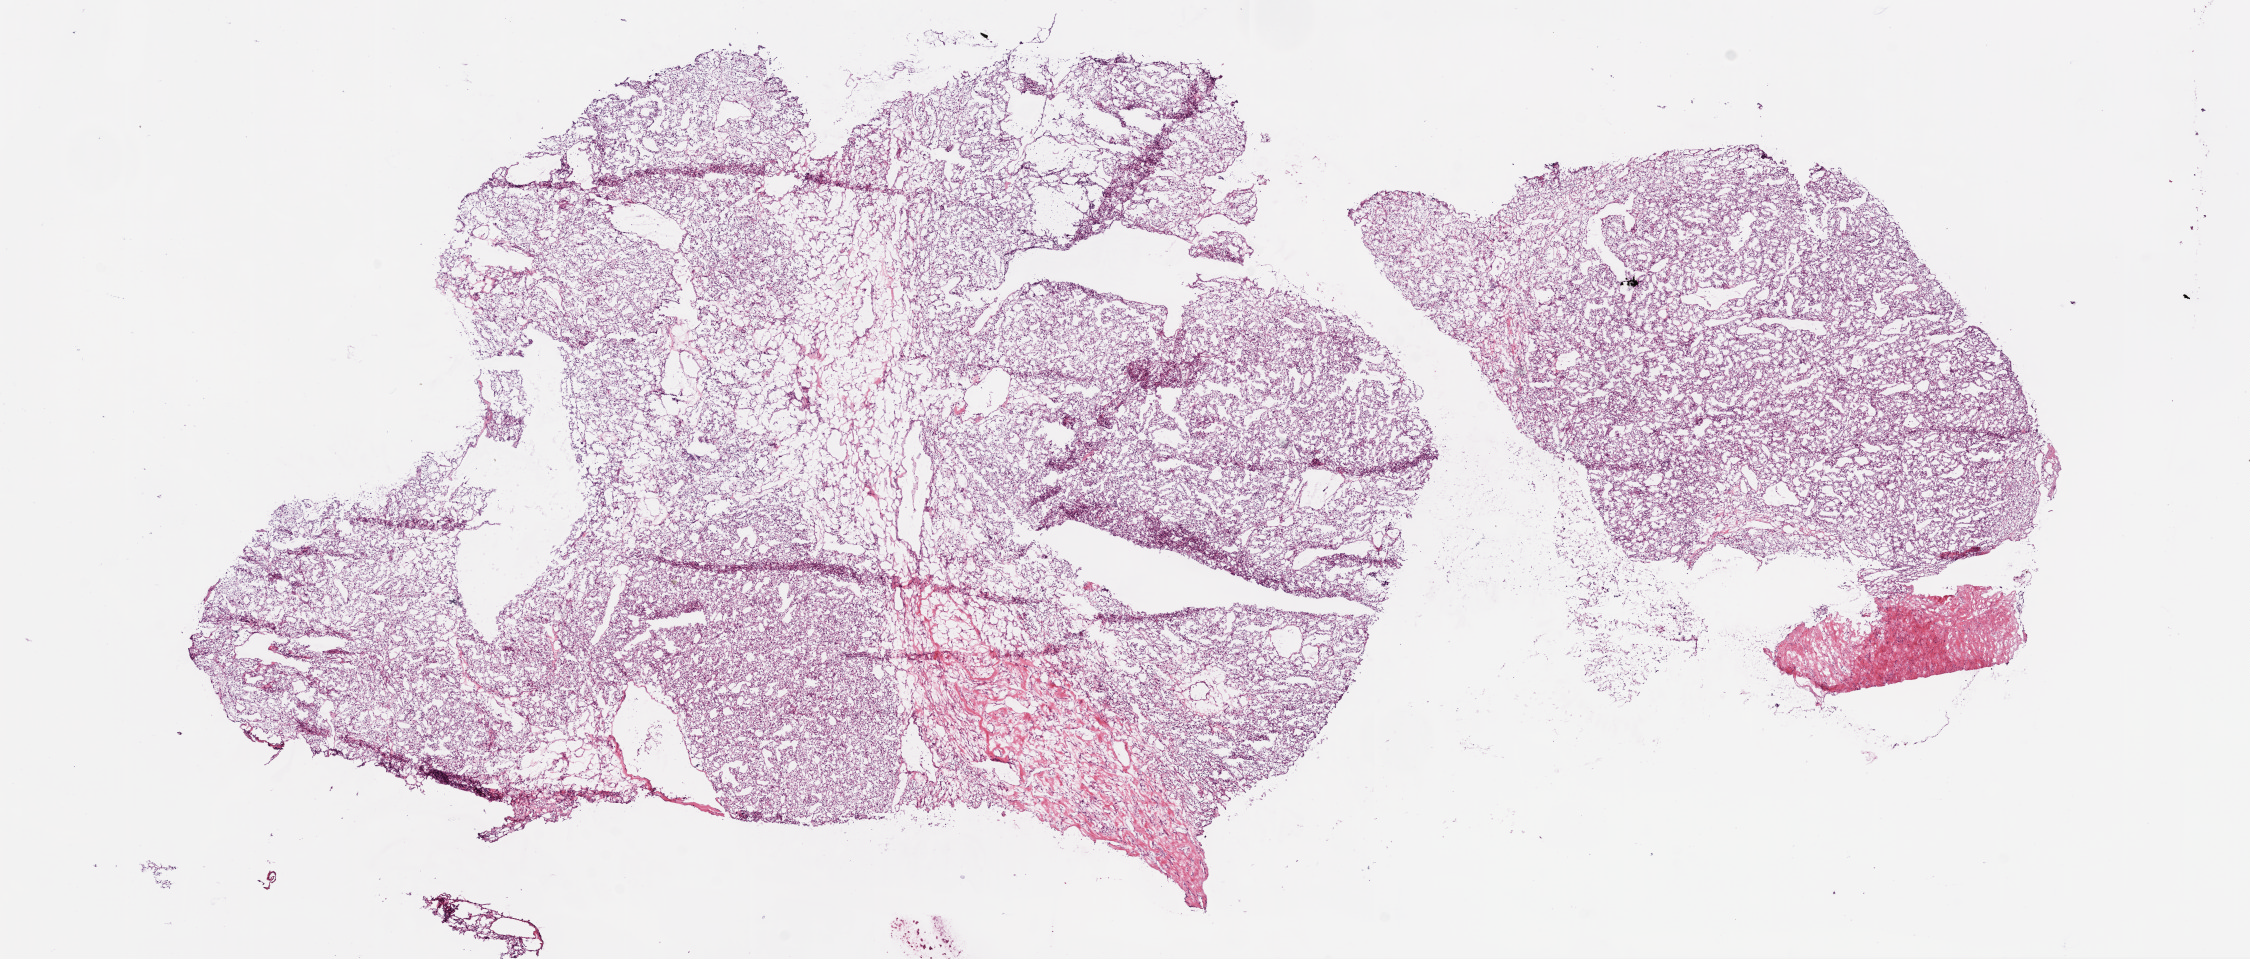
Whole-slide histology image, H&E-stained — a low-resolution overview of the entire scanned area, about 18.1 x 7.7 mm (from a 20x scan), frozen section from the bottom of the tissue portion, primary tumour sample from the kidney. Patient: male, age at initial diagnosis 45 years. Histologic grade: G2 (moderately differentiated). Slide review estimates, as recorded: tumour cells 85%, tumour nuclei 80%, normal cells 0%, stromal cells 15%, necrosis 0%.
* diagnosis: Clear cell adenocarcinoma, NOS
* AJCC pathologic stage: II